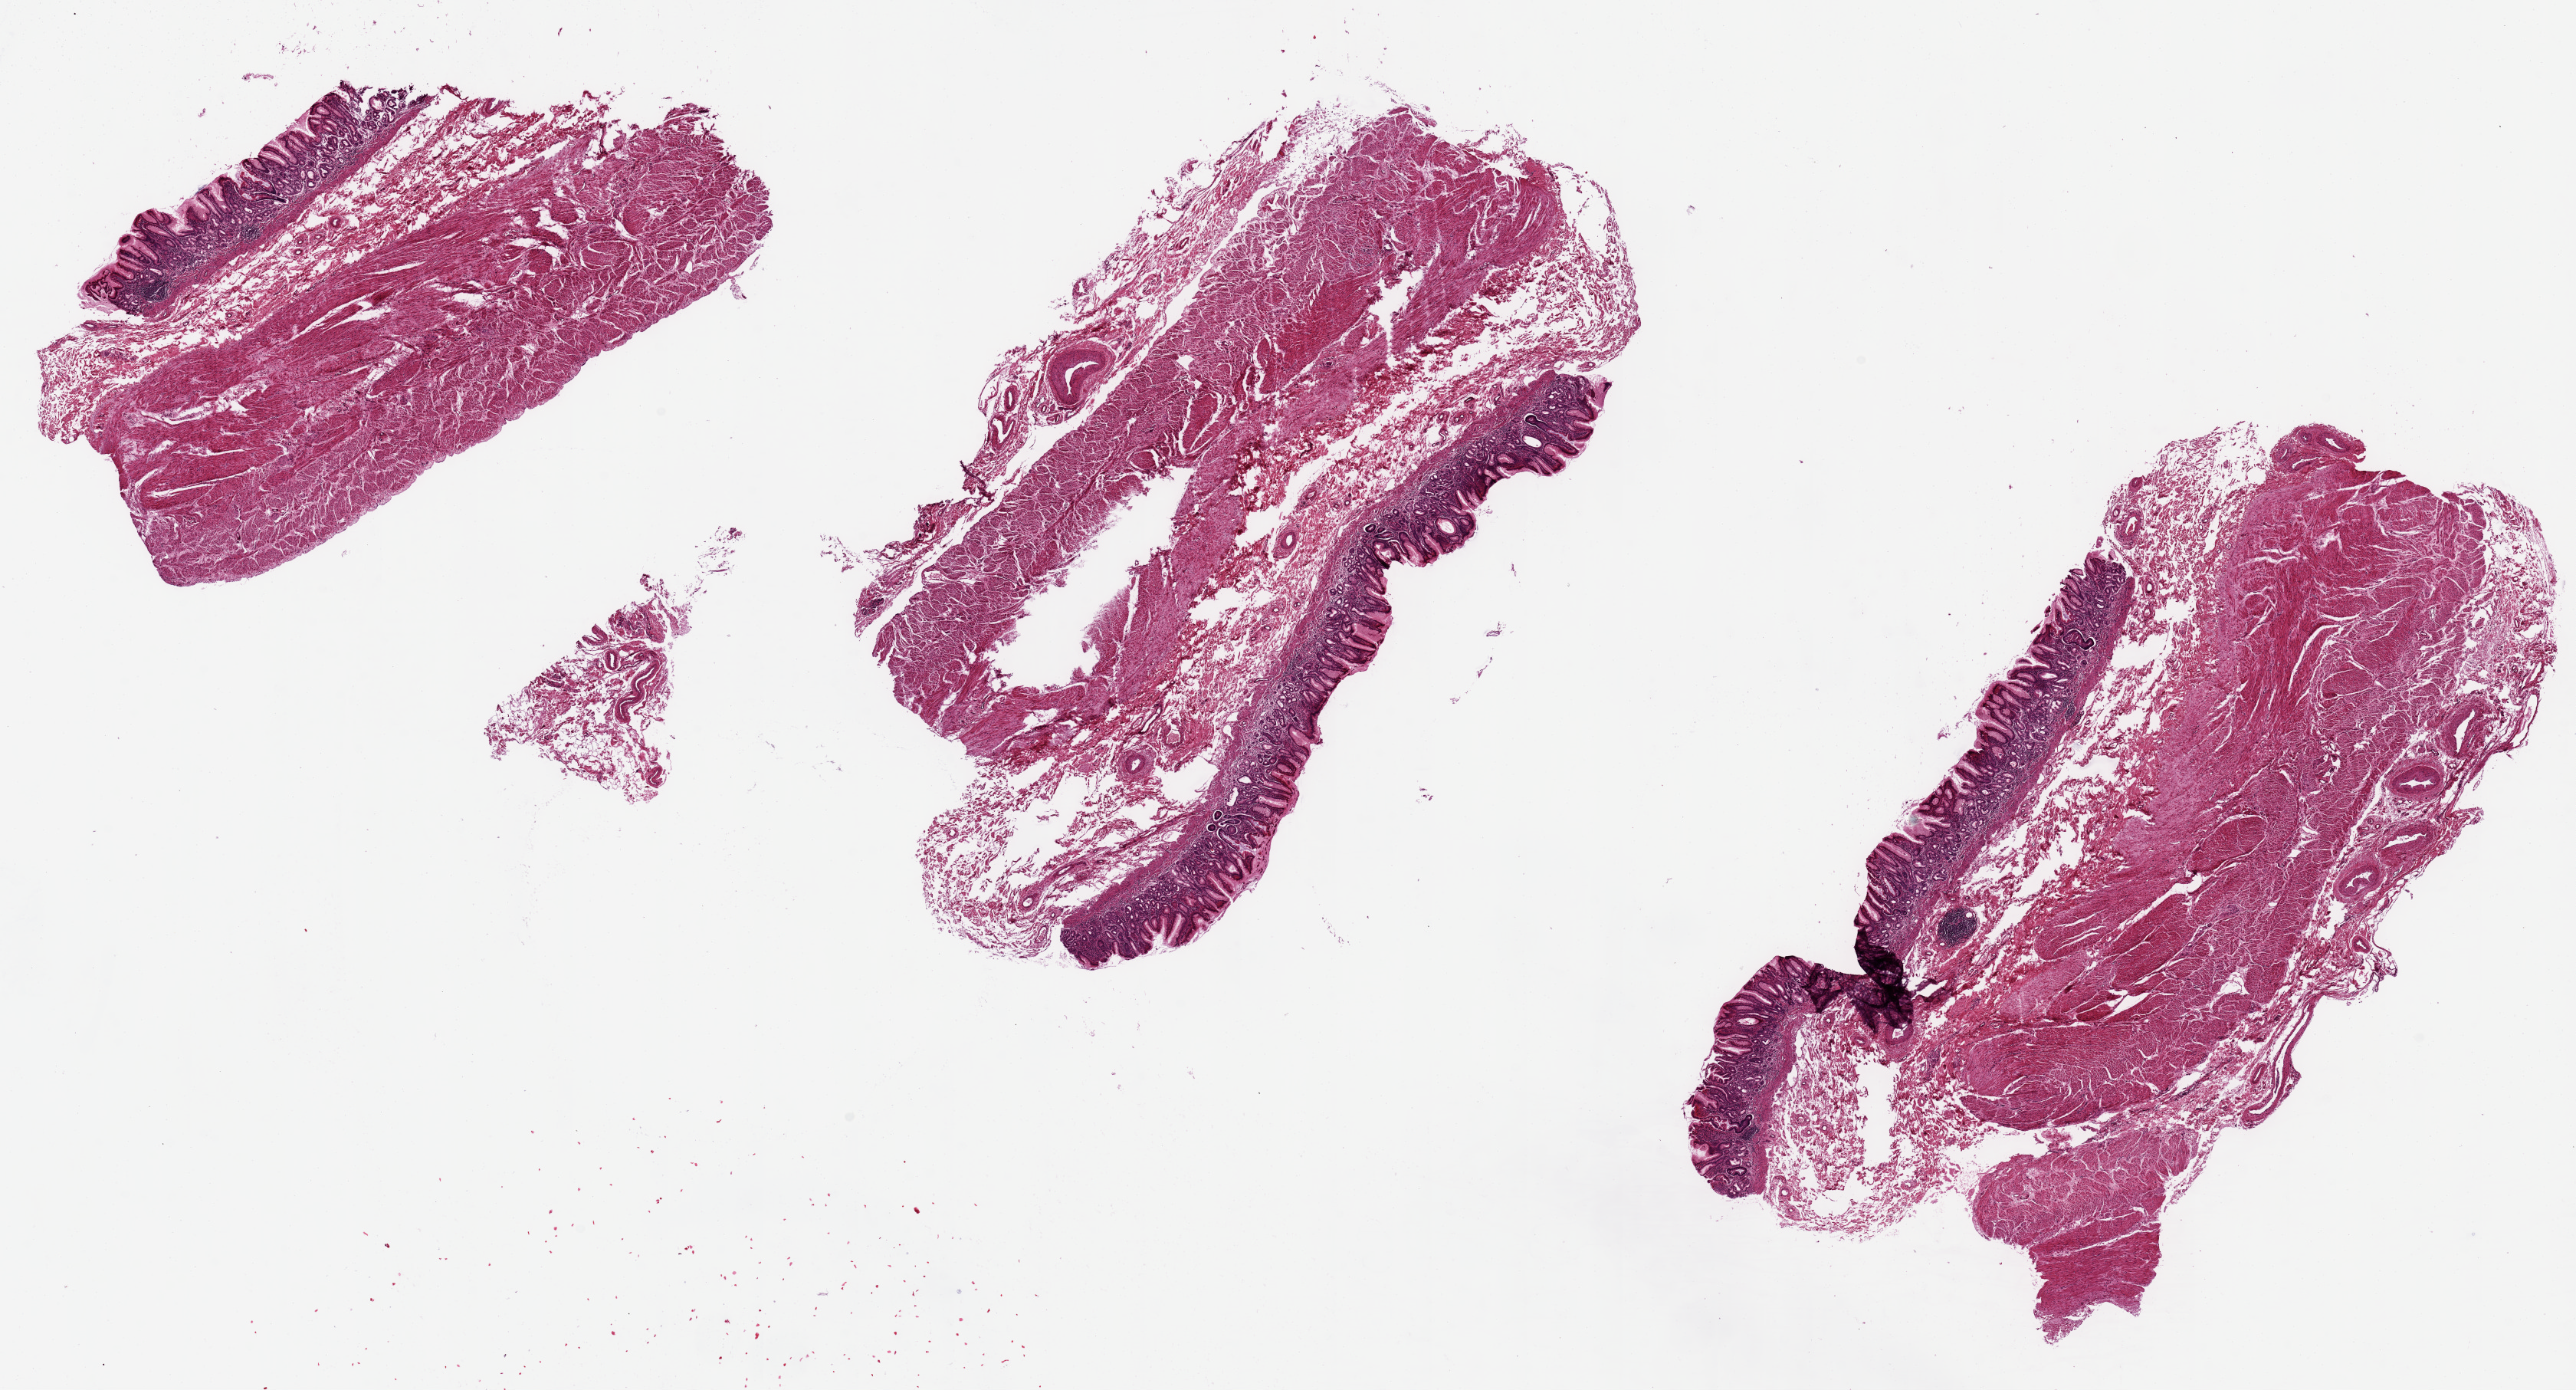
Whole-slide image, H&E stain — whole scanned area (about 26.6 x 14.3 mm, slide scanned at 20x) shown as a low-resolution overview. PAXgene-fixed, paraffin-embedded tissue. Sampled site (target tissue): stomach. Donor tissue sample. Donor: female.
Reviewer comment on this tissue sample: Chronic gastritis, intestinal metaplasia; antral mucosa.